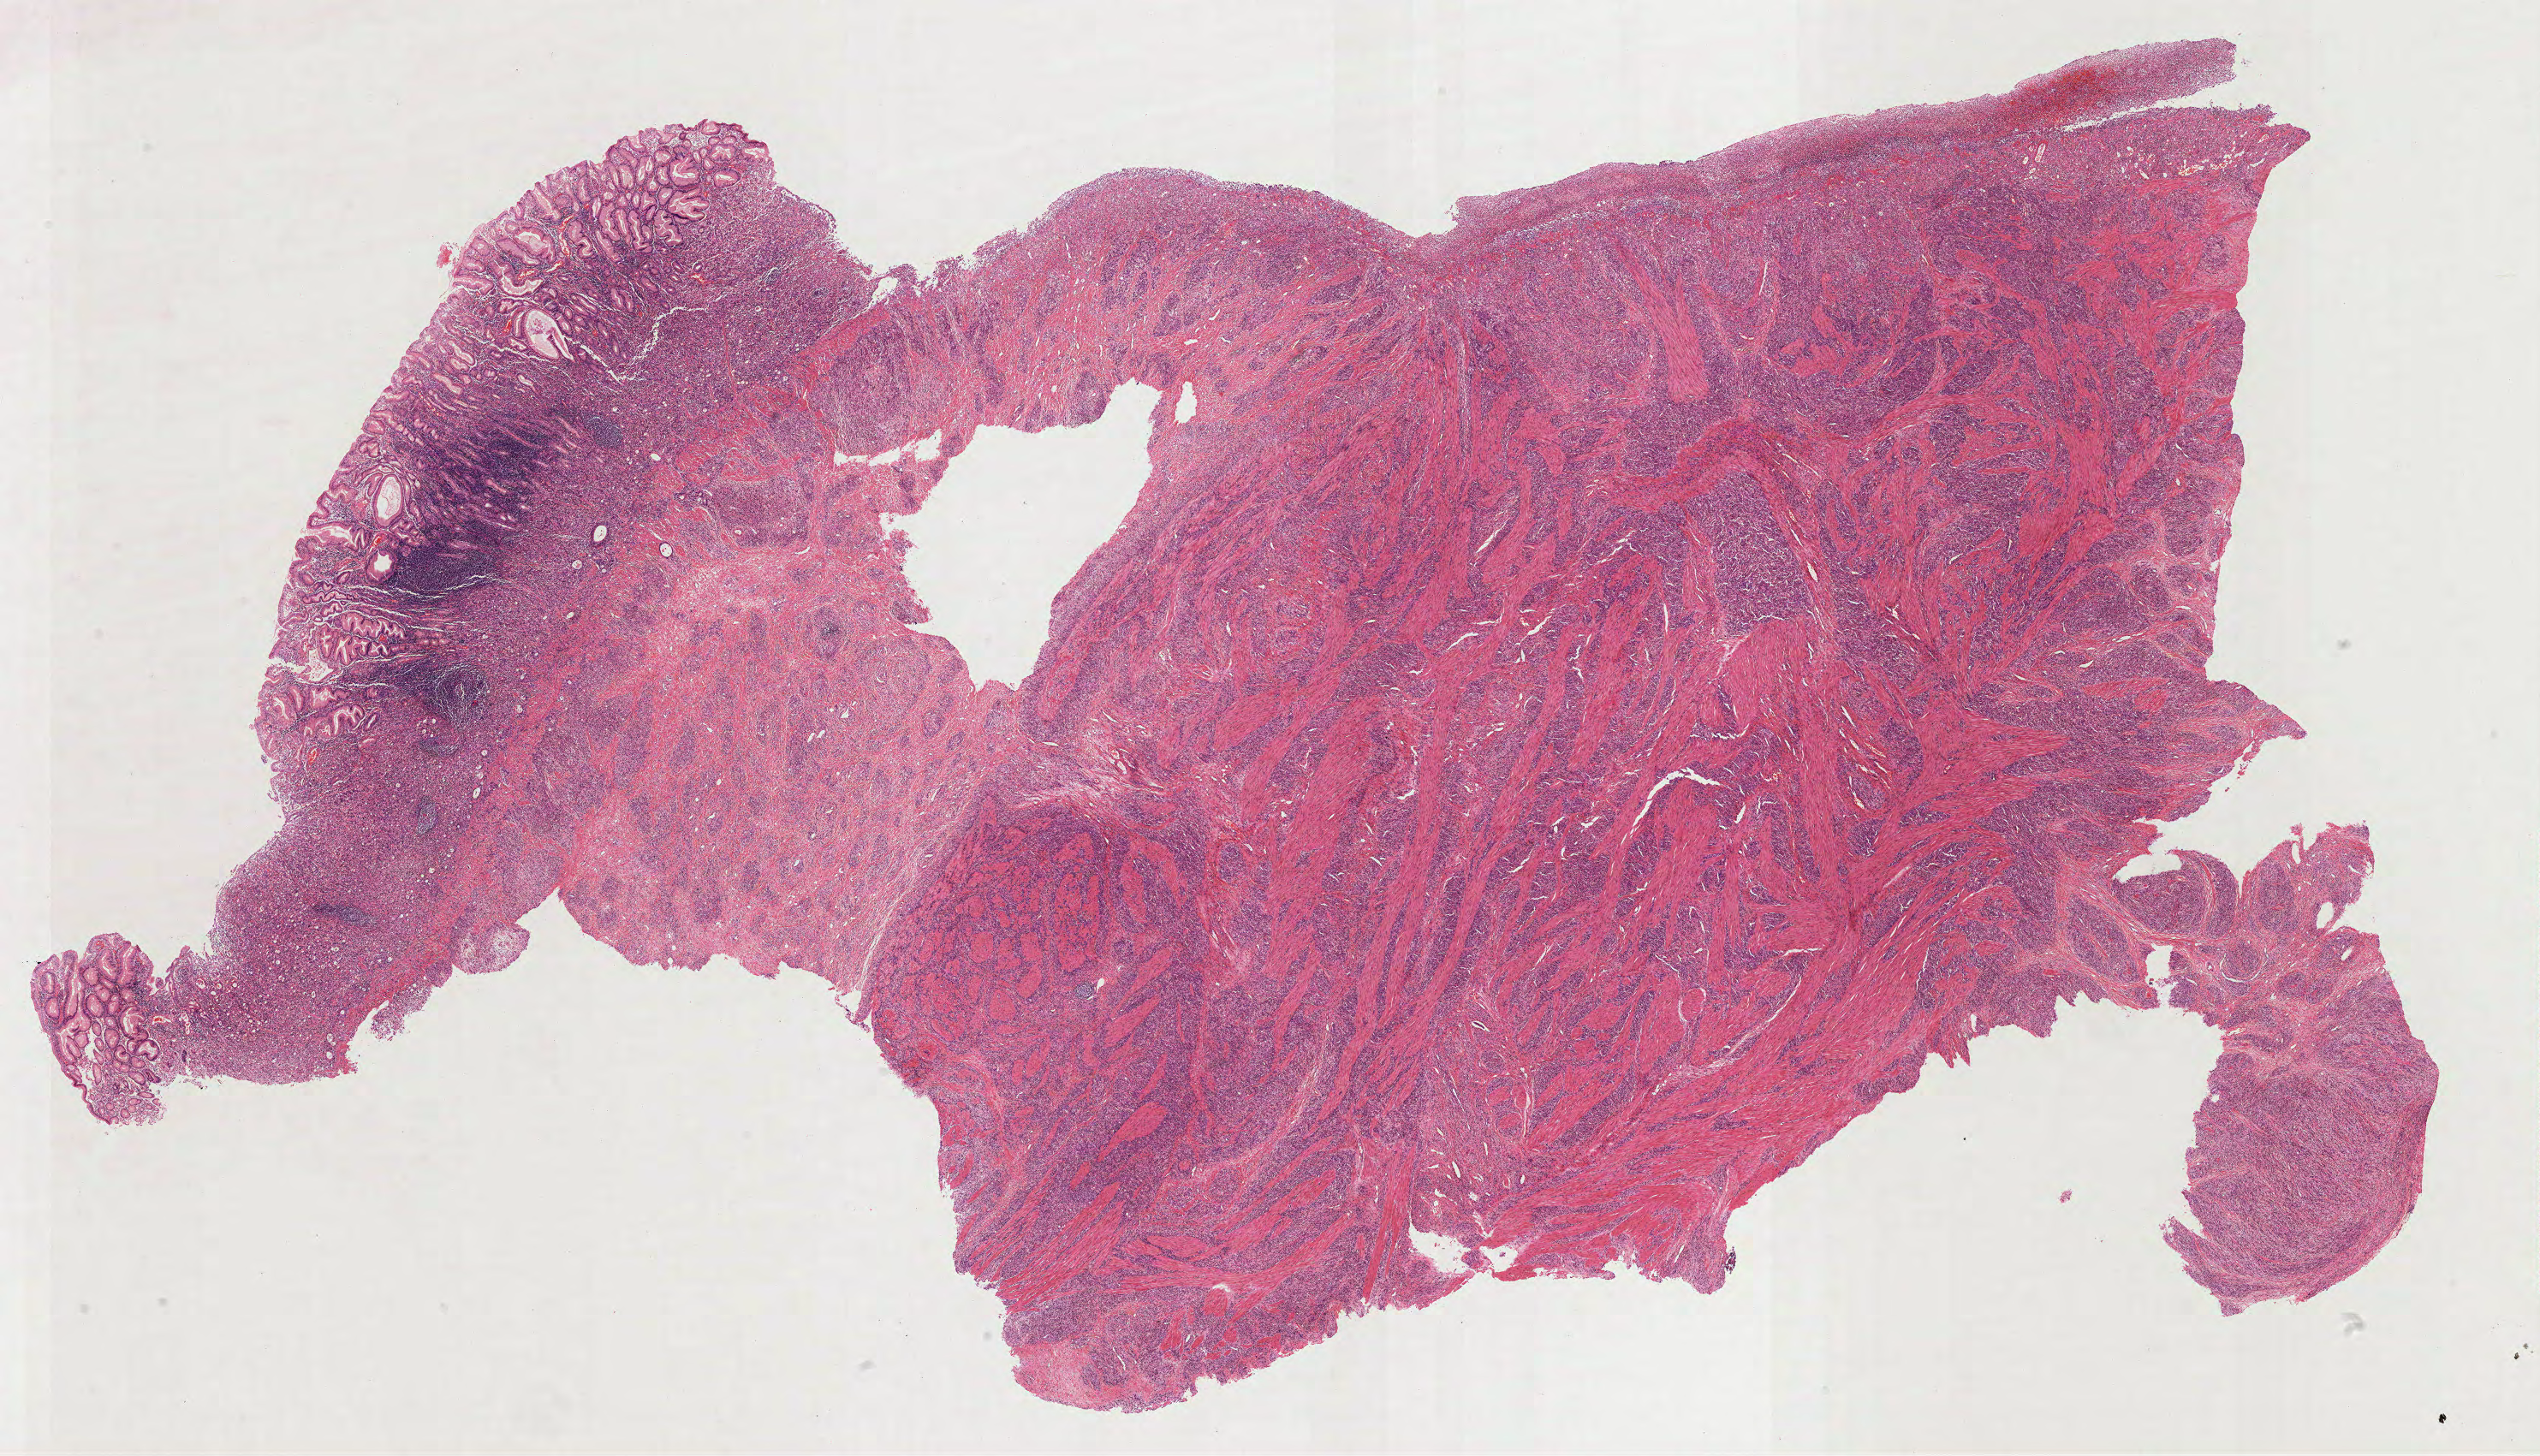
Digitized H&E-stained tissue section (whole slide) — whole scanned area (about 23.9 x 13.7 mm, from a 40x scan) shown as a low-resolution overview; formalin-fixed paraffin-embedded (FFPE) diagnostic section; stomach, primary tumour sample. Male patient; age at initial diagnosis 55 years. Histologic grade: G3 (poorly differentiated).
AJCC pathologic stage: IIIB (7th edition). Diagnosis: Adenocarcinoma, NOS (fundus of stomach). Lymph nodes positive (case pathology): 9 of 15 examined.